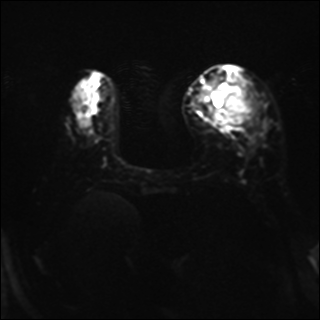
Breast MRI, one axial slice; position 11 of 37 along the scan axis; diffusion-weighted series; image 2 of 4 stored at this slice position (different b-values; order by instance number); 1.5 T; 4 mm slice thickness; 320 × 320 image matrix, field of view 320 × 320 mm. Female patient.
Annotated regions visible in this slice (outlined manually by an expert reader):
- tumour on diffusion-weighted imaging: box from (x=213, y=83) to (x=256, y=126) px